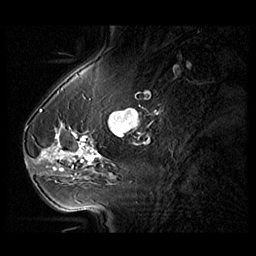
Breast MRI (dynamic contrast-enhanced), one sagittal slice. Position 35 of 104 along the scan axis. 3 images stored at this slice position (order not interpretable as contrast timing). 1.5 T. TE 1.3 ms, TR 5.5 ms. 256 × 256 image matrix. Female patient, age 54 years. Case-level facts recorded for this patient, not image findings: setting: breast cancer imaged before/during neoadjuvant chemotherapy; receptor status: HR-positive, HER2-negative.
Outlined on this slice (semi-automatic segmentation, software-assisted and operator-edited):
- analysis volume of interest (the breast-tissue region the enhancement analysis was run in; not a lesion): bounding box (x1, y1, x2, y2) in pixels: (28, 127, 104, 182)
- tumour enhancement mask (voxels above the 140 % enhancement threshold inside the analysis volume of interest): (39, 133, 98, 171)